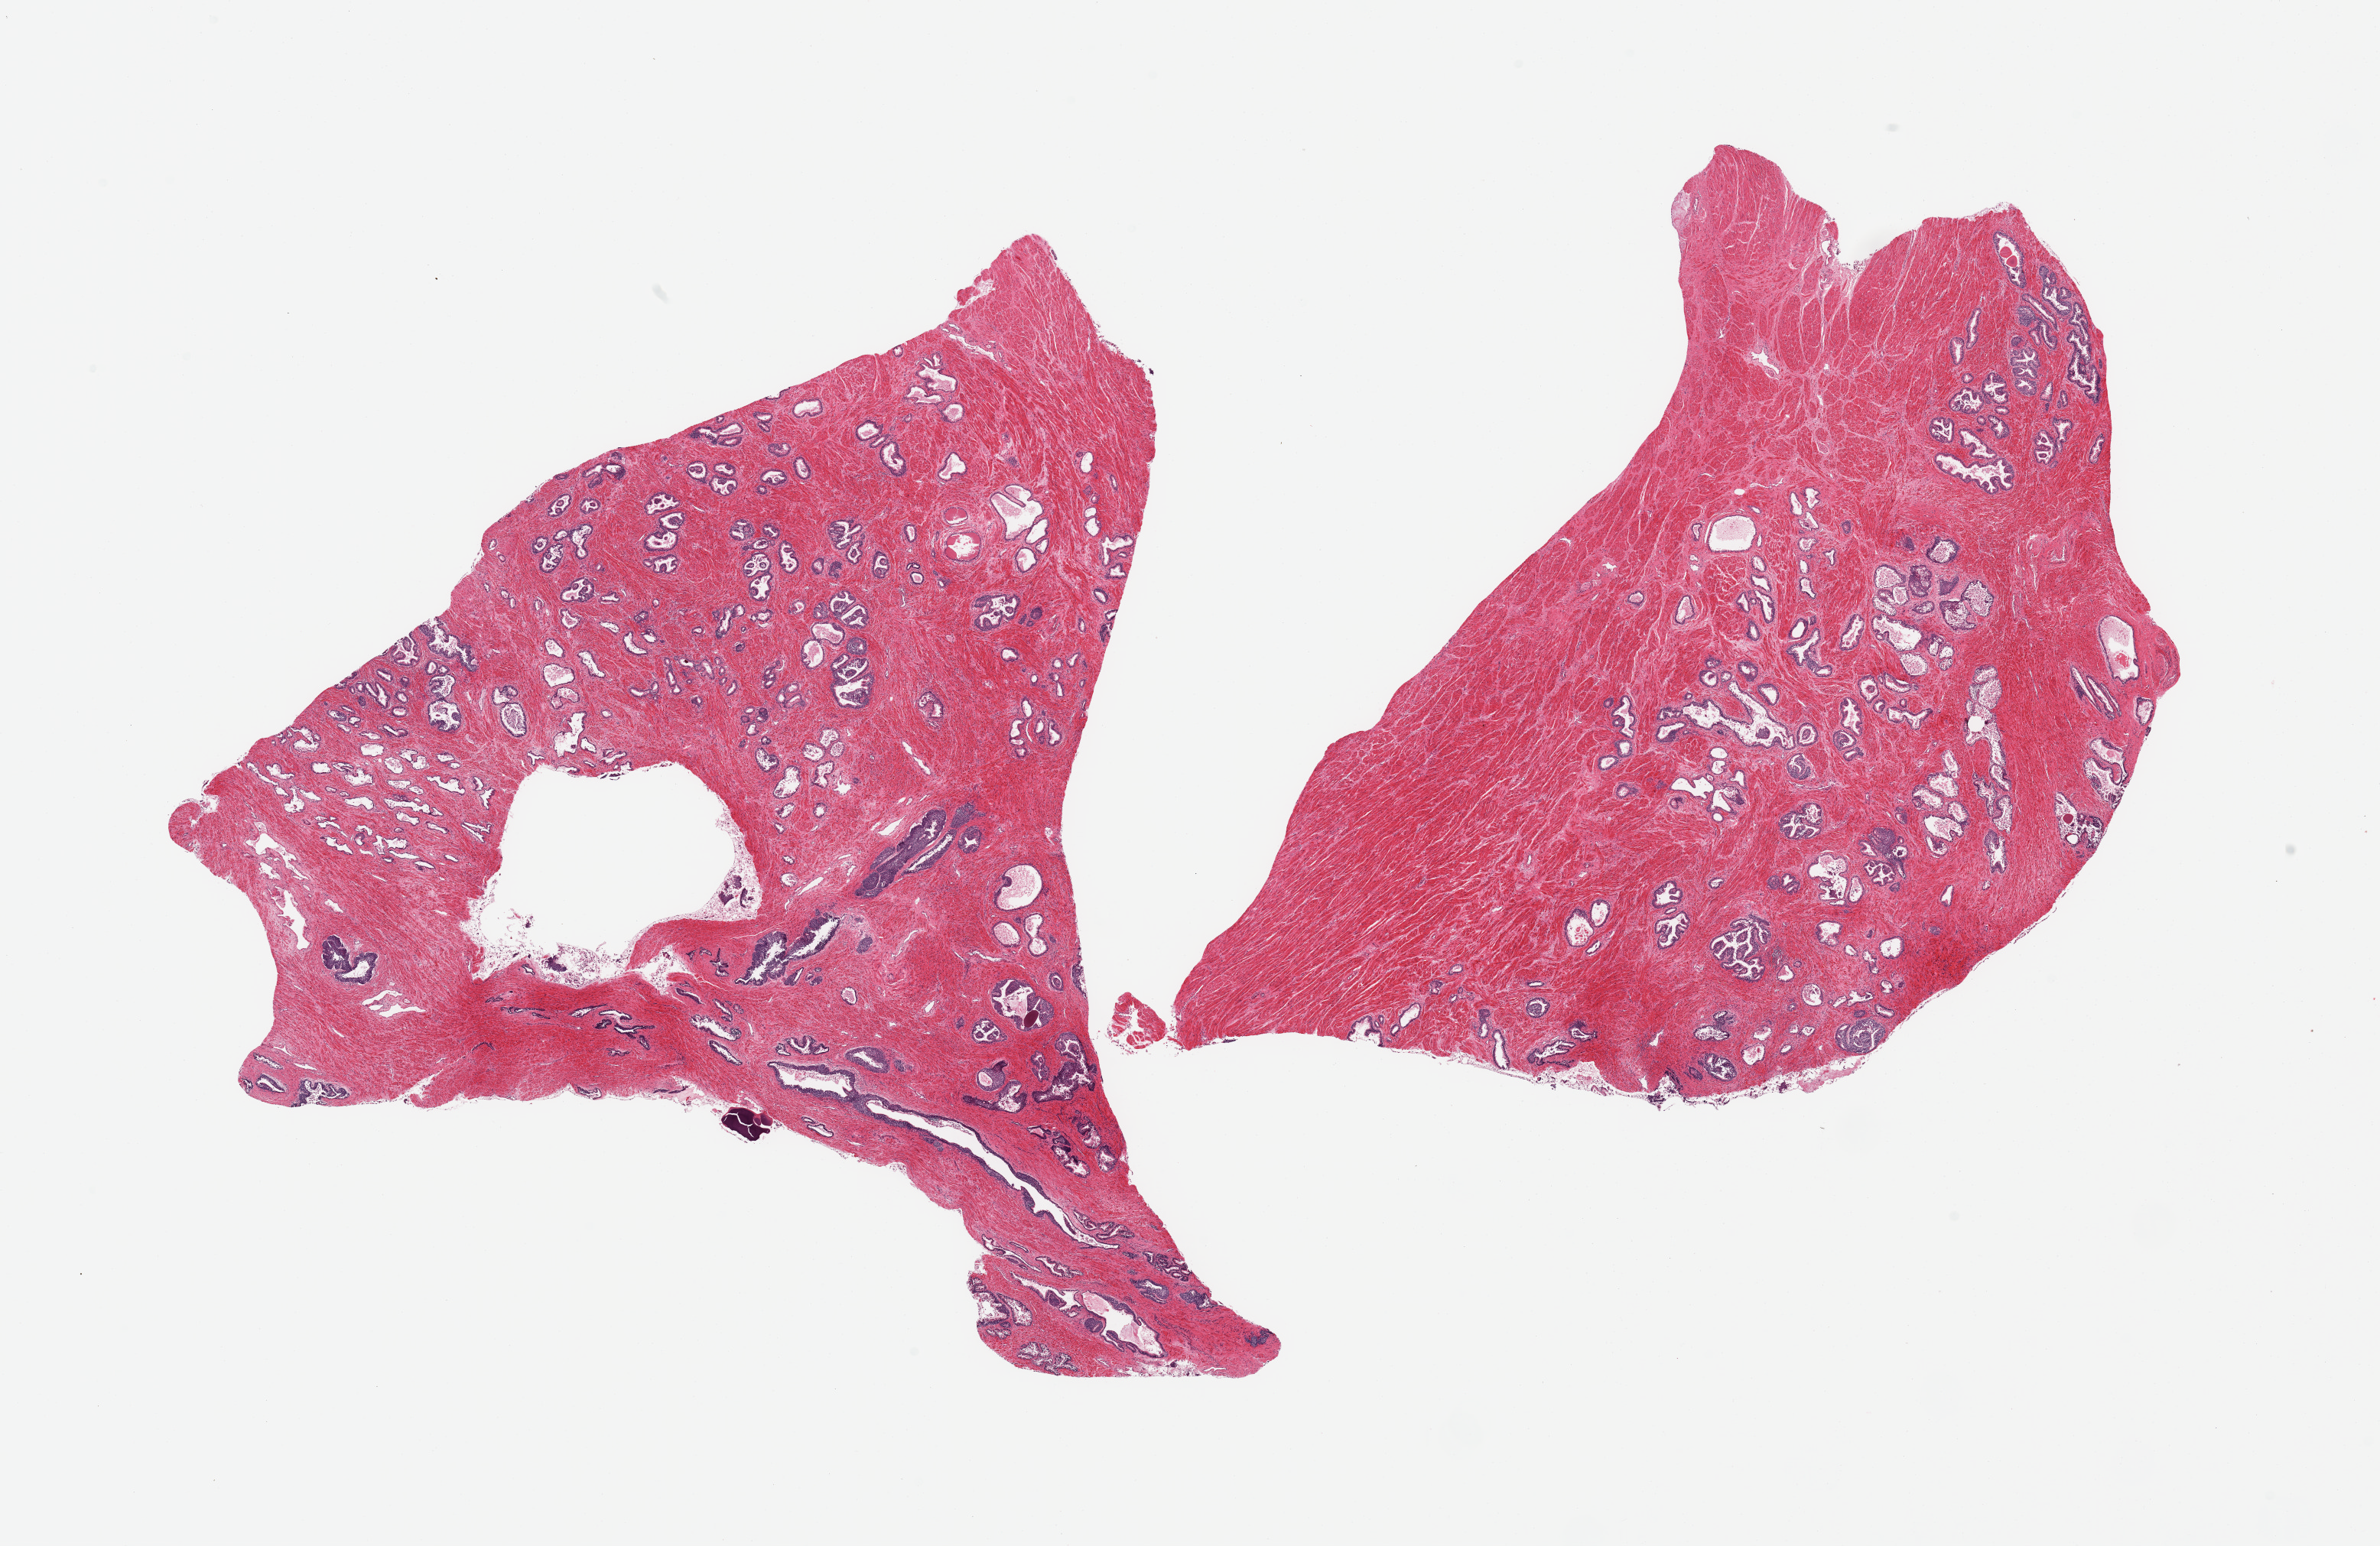
Whole-slide image, H&E stain — low-resolution overview of the scanned area, about 24.6 x 16.0 mm; PAXgene-fixed paraffin-embedded (PFPE) section; section of prostate (target tissue); donor tissue sample. Donor: male.
Review note (as recorded): 2 pieces; fibromuscular stroma and glands, some periurethral ducts/glands.